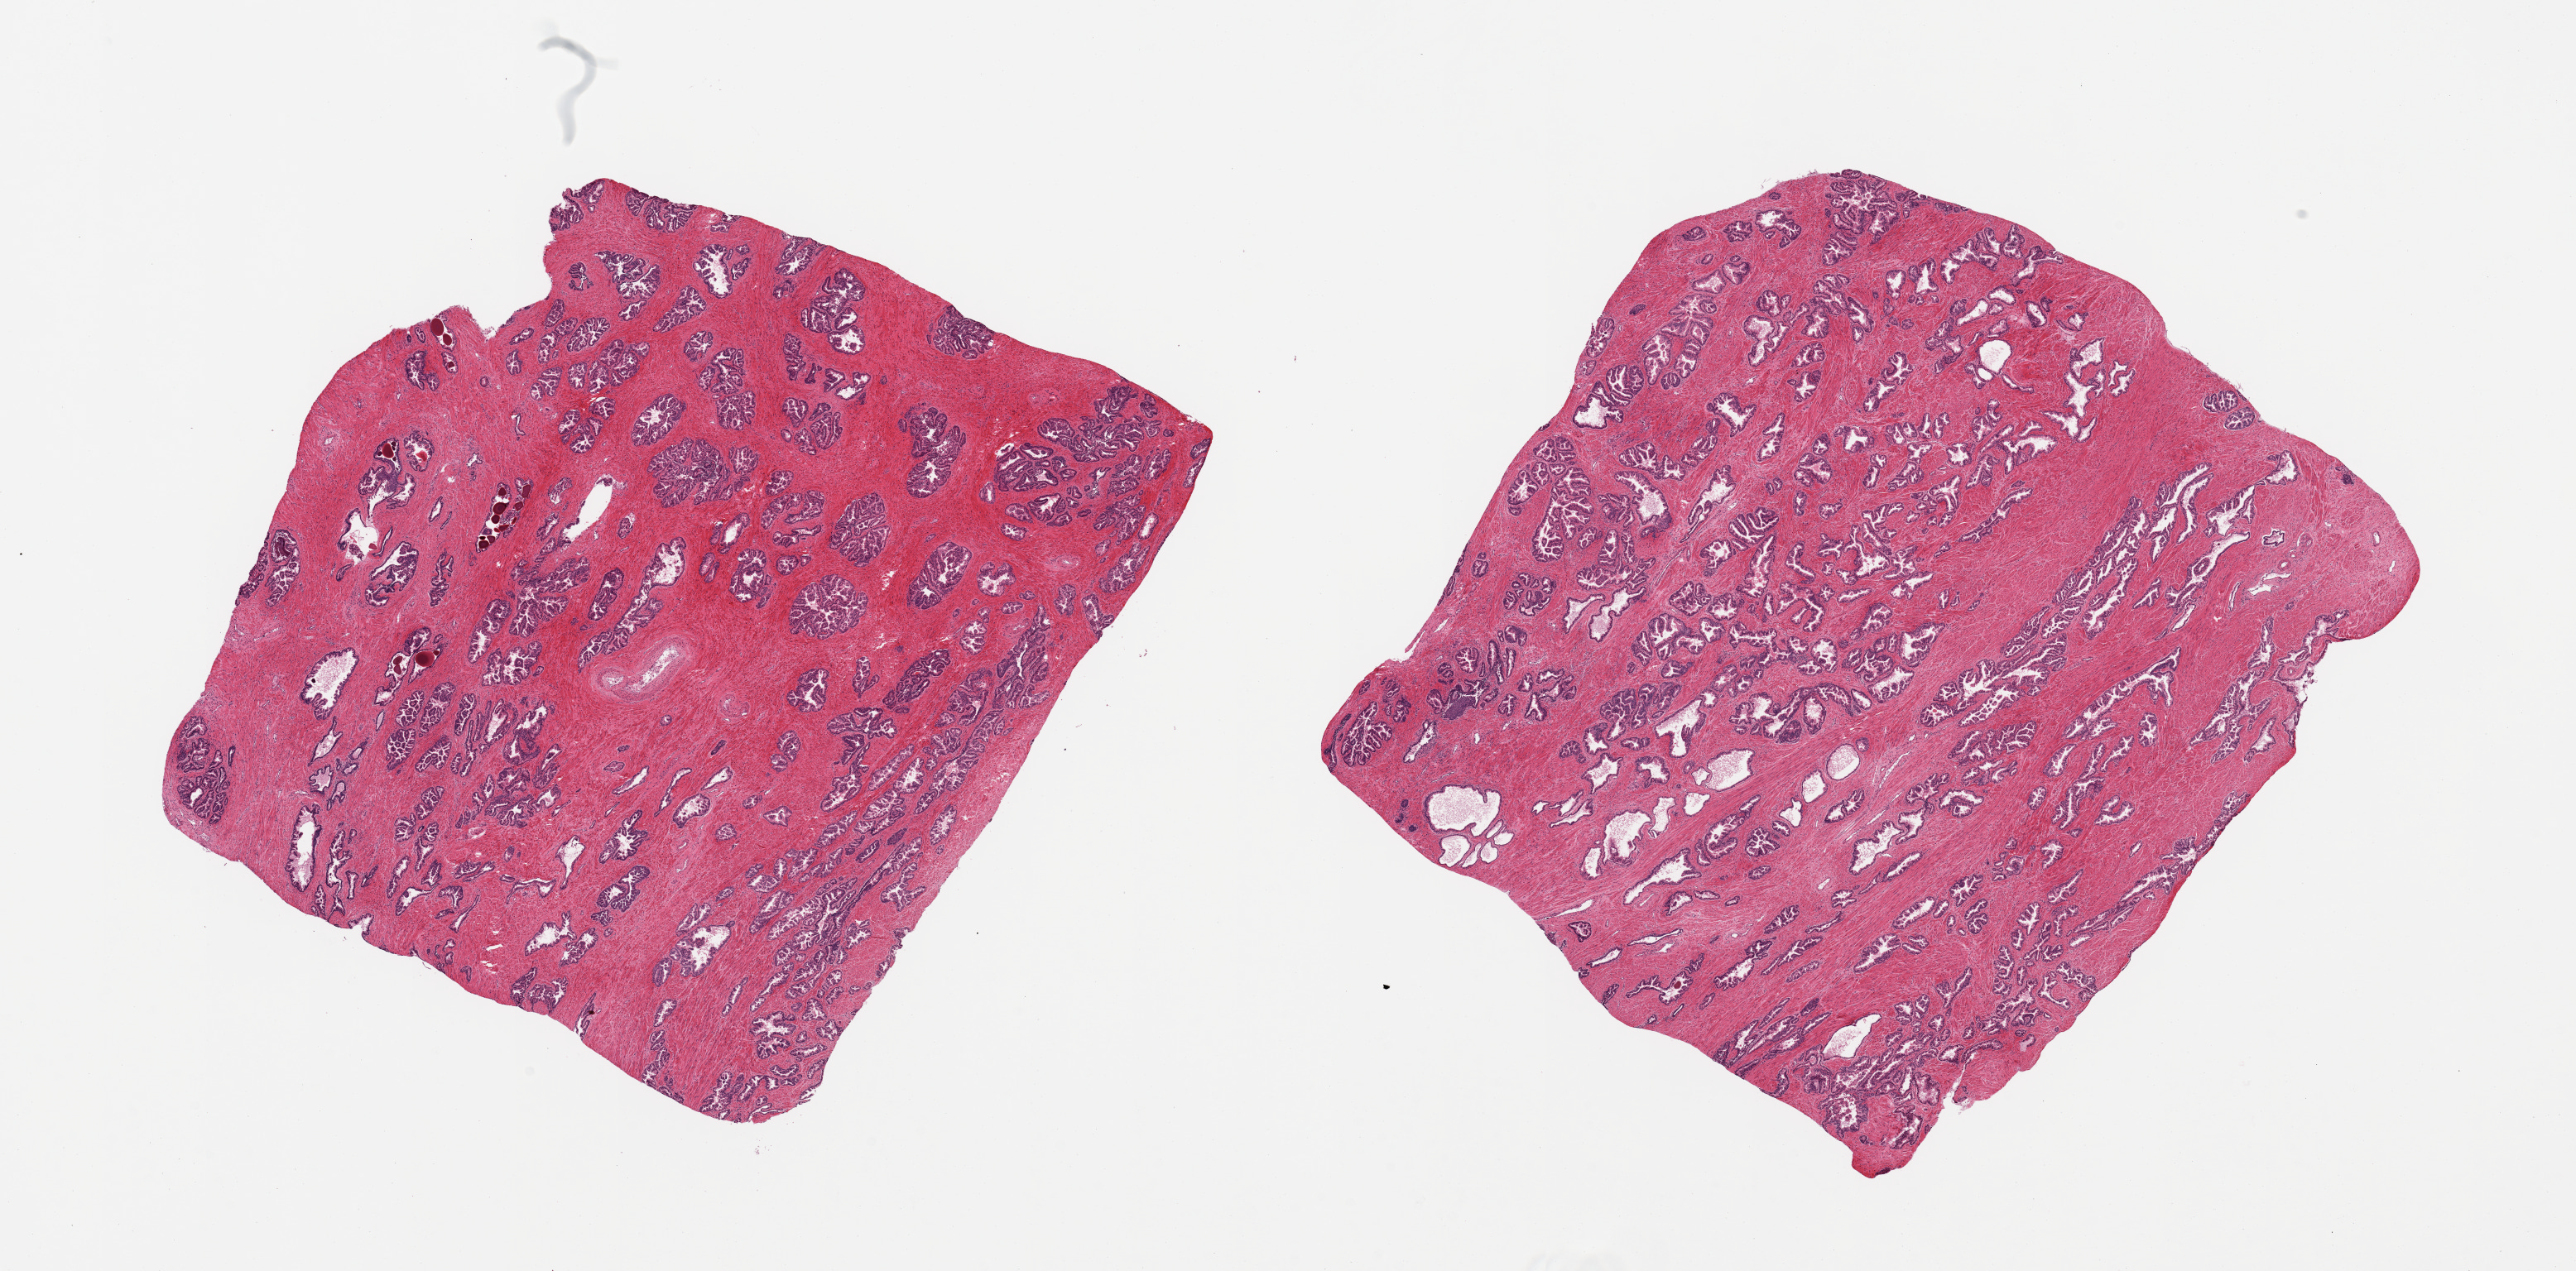
Whole-slide image, haematoxylin and eosin stain, brightfield — shown as a low-resolution overview of the whole scanned area (about 24.6 x 12.1 mm, from a 20x scan). PAXgene-fixed, paraffin-embedded tissue. Section of prostate (target tissue). Tissue donor sample. Donor: male.
Pathologist's review note for this sample: 2 pieces; well preserved fibromuscular stroma and glandular component.